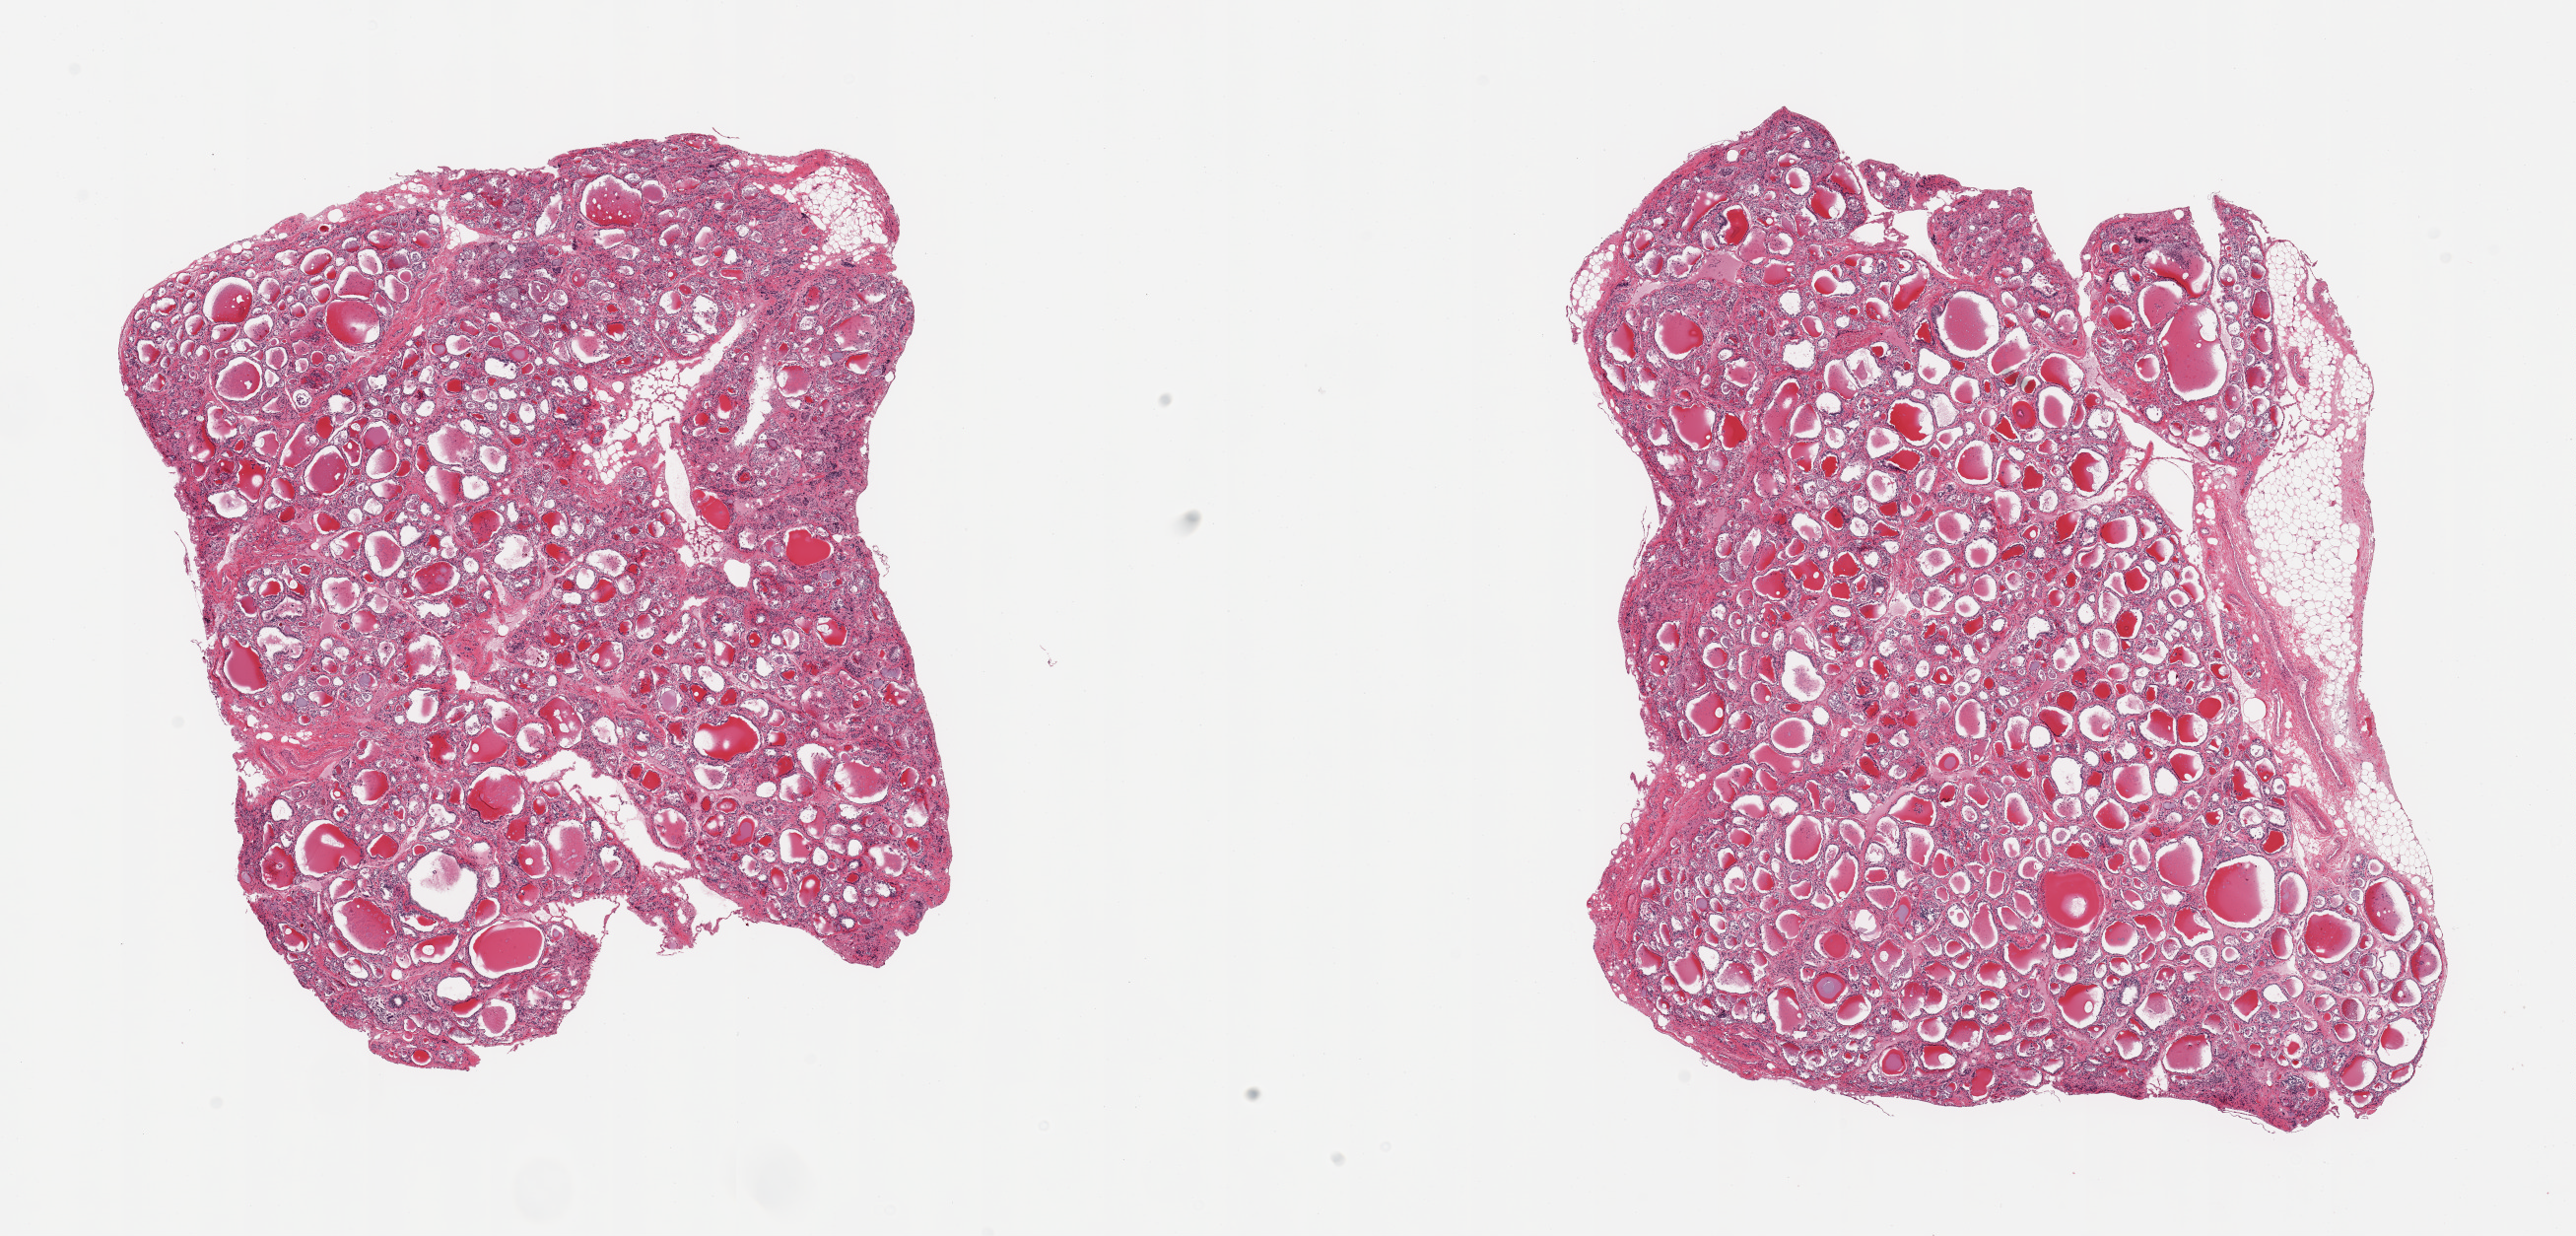
Whole-slide image, haematoxylin and eosin stain, low-resolution overview of the scanned area, about 20.7 x 9.9 mm (from a 20x scan); PAXgene-fixed paraffin-embedded (PFPE) section; section of thyroid (target tissue); tissue donor sample. Male donor.
Reviewer comment on this tissue sample: 2 pieces, mild thryoiditis.